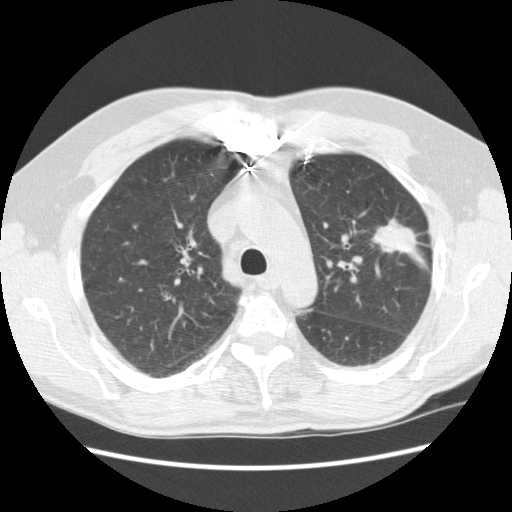
Low-dose screening chest CT, one axial slice. Slice 172 of 231 in the series (ordered by position). Reconstruction kernel STANDARD. Lung window (W 1500 / L -600 HU). 2.5 mm slice thickness. 512 × 512 image matrix, field of view 362 × 362 mm.
Structures marked on this image (expert manual segmentation):
- lesion 1 (tumor, upper lobe of left lung): bounding box [x1, y1, x2, y2] px = [373, 219, 418, 253]